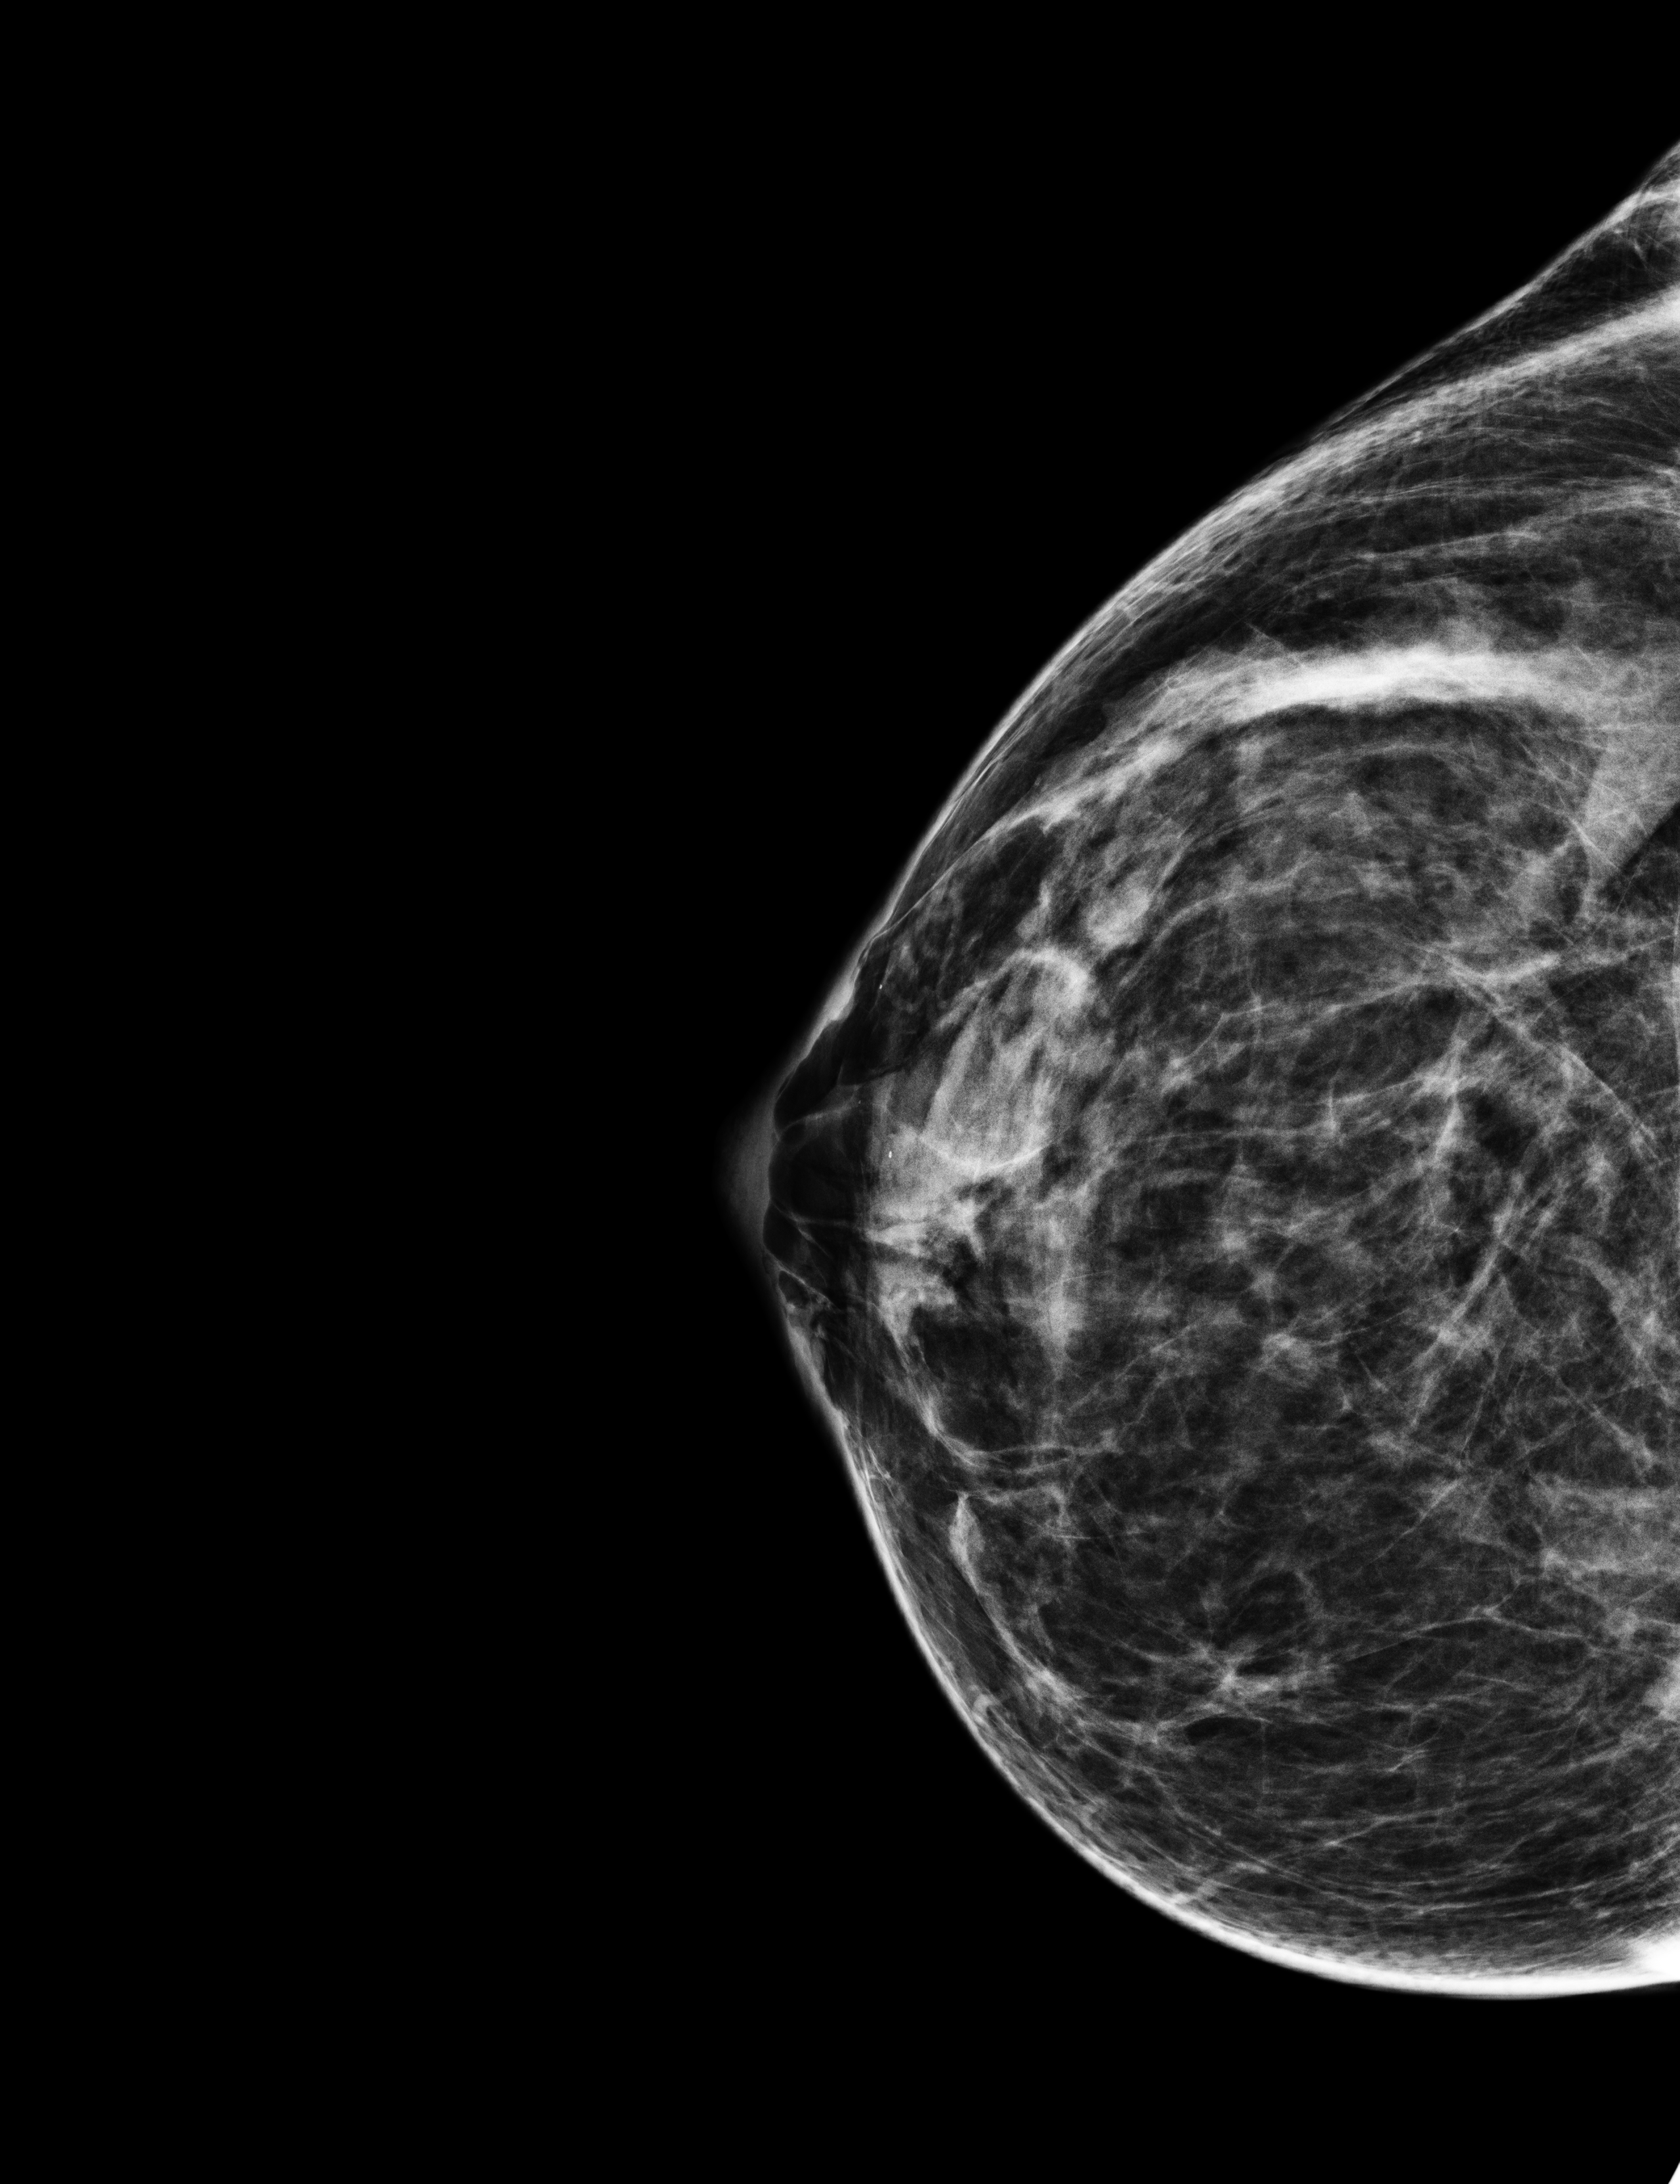
Annual screening mammography examination. Female patient, age 45 years.
Image type: full-field digital mammogram. Breast: right. Projection: CC view.